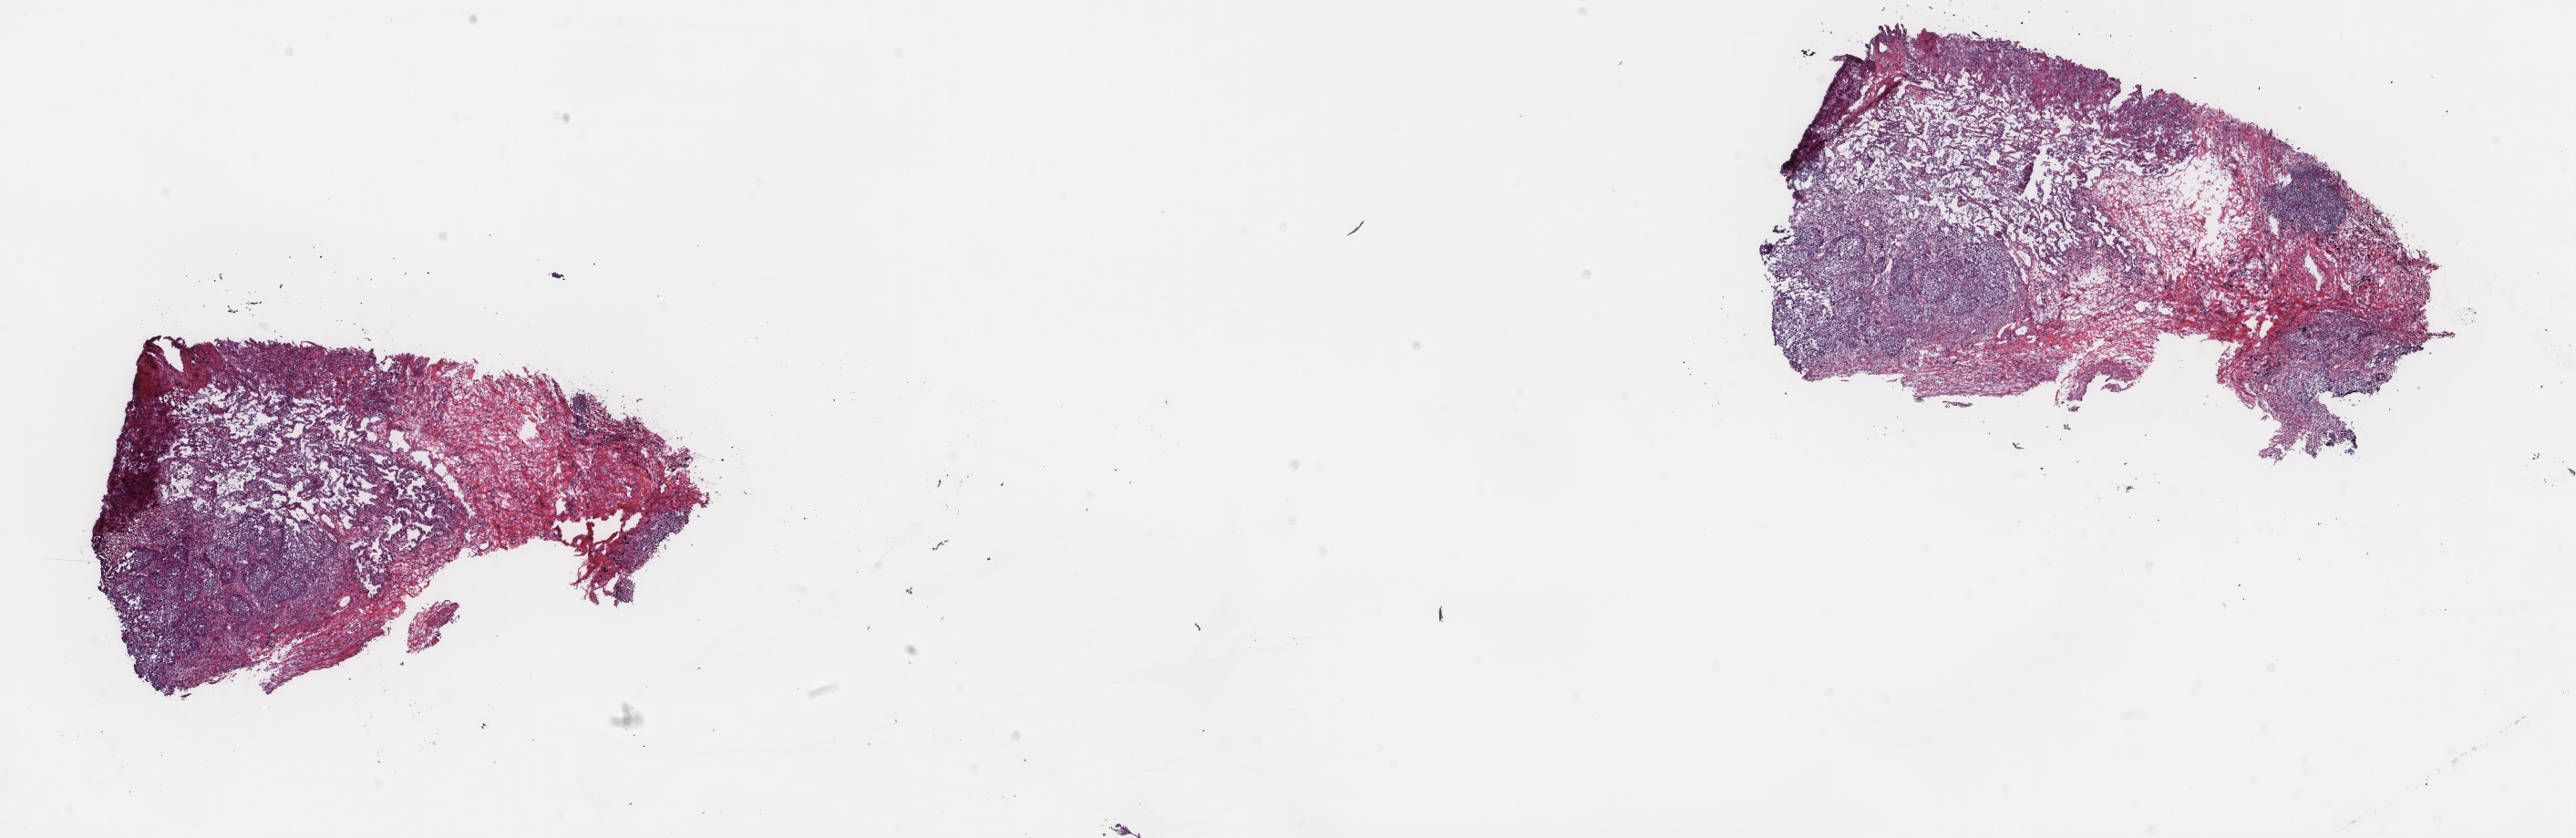
Hematoxylin and eosin (H&E) stained whole-slide image, shown as a low-resolution overview of the whole scanned area (about 22.4 x 7.3 mm, acquisition: 40x scan); frozen section from the top of the tissue portion; sample: primary tumour, lung. Male patient; age at initial diagnosis 69 years. Composition of this section per pathologist review: tumour cells 25%, tumour nuclei 90%, normal cells 50%, stromal cells 25%, necrosis 0%. Inflammatory infiltration, as recorded: lymphocyte infiltration 20%, monocyte infiltration 10%, neutrophil infiltration 0%.
Pathologic diagnosis: Squamous cell carcinoma, NOS (upper lobe, lung). AJCC pathologic stage: IB (7th edition).